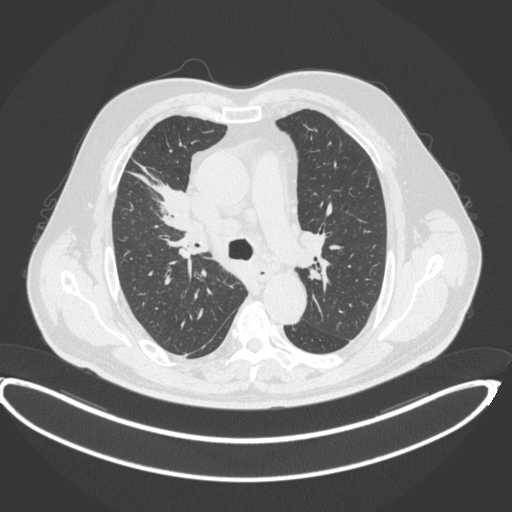
Chest CT, one axial slice; slice 273 of 395 in the series (ordered by position); reconstruction kernel B31f; 120 kVp; lung window (W 1500 / L -600 HU); 1 mm slice thickness; 512 × 512 image matrix, field of view 448 × 448 mm. Patient: male, 62 years. Case-level facts recorded for this patient, not image findings: clinical TNM (as recorded): T1c N3 M1c.
Outlined on this slice (bounding box drawn by a radiologist):
- lung tumour (recorded histology: adenocarcinoma): bounding box <130,164,197,230> (left, top, right, bottom; pixels)